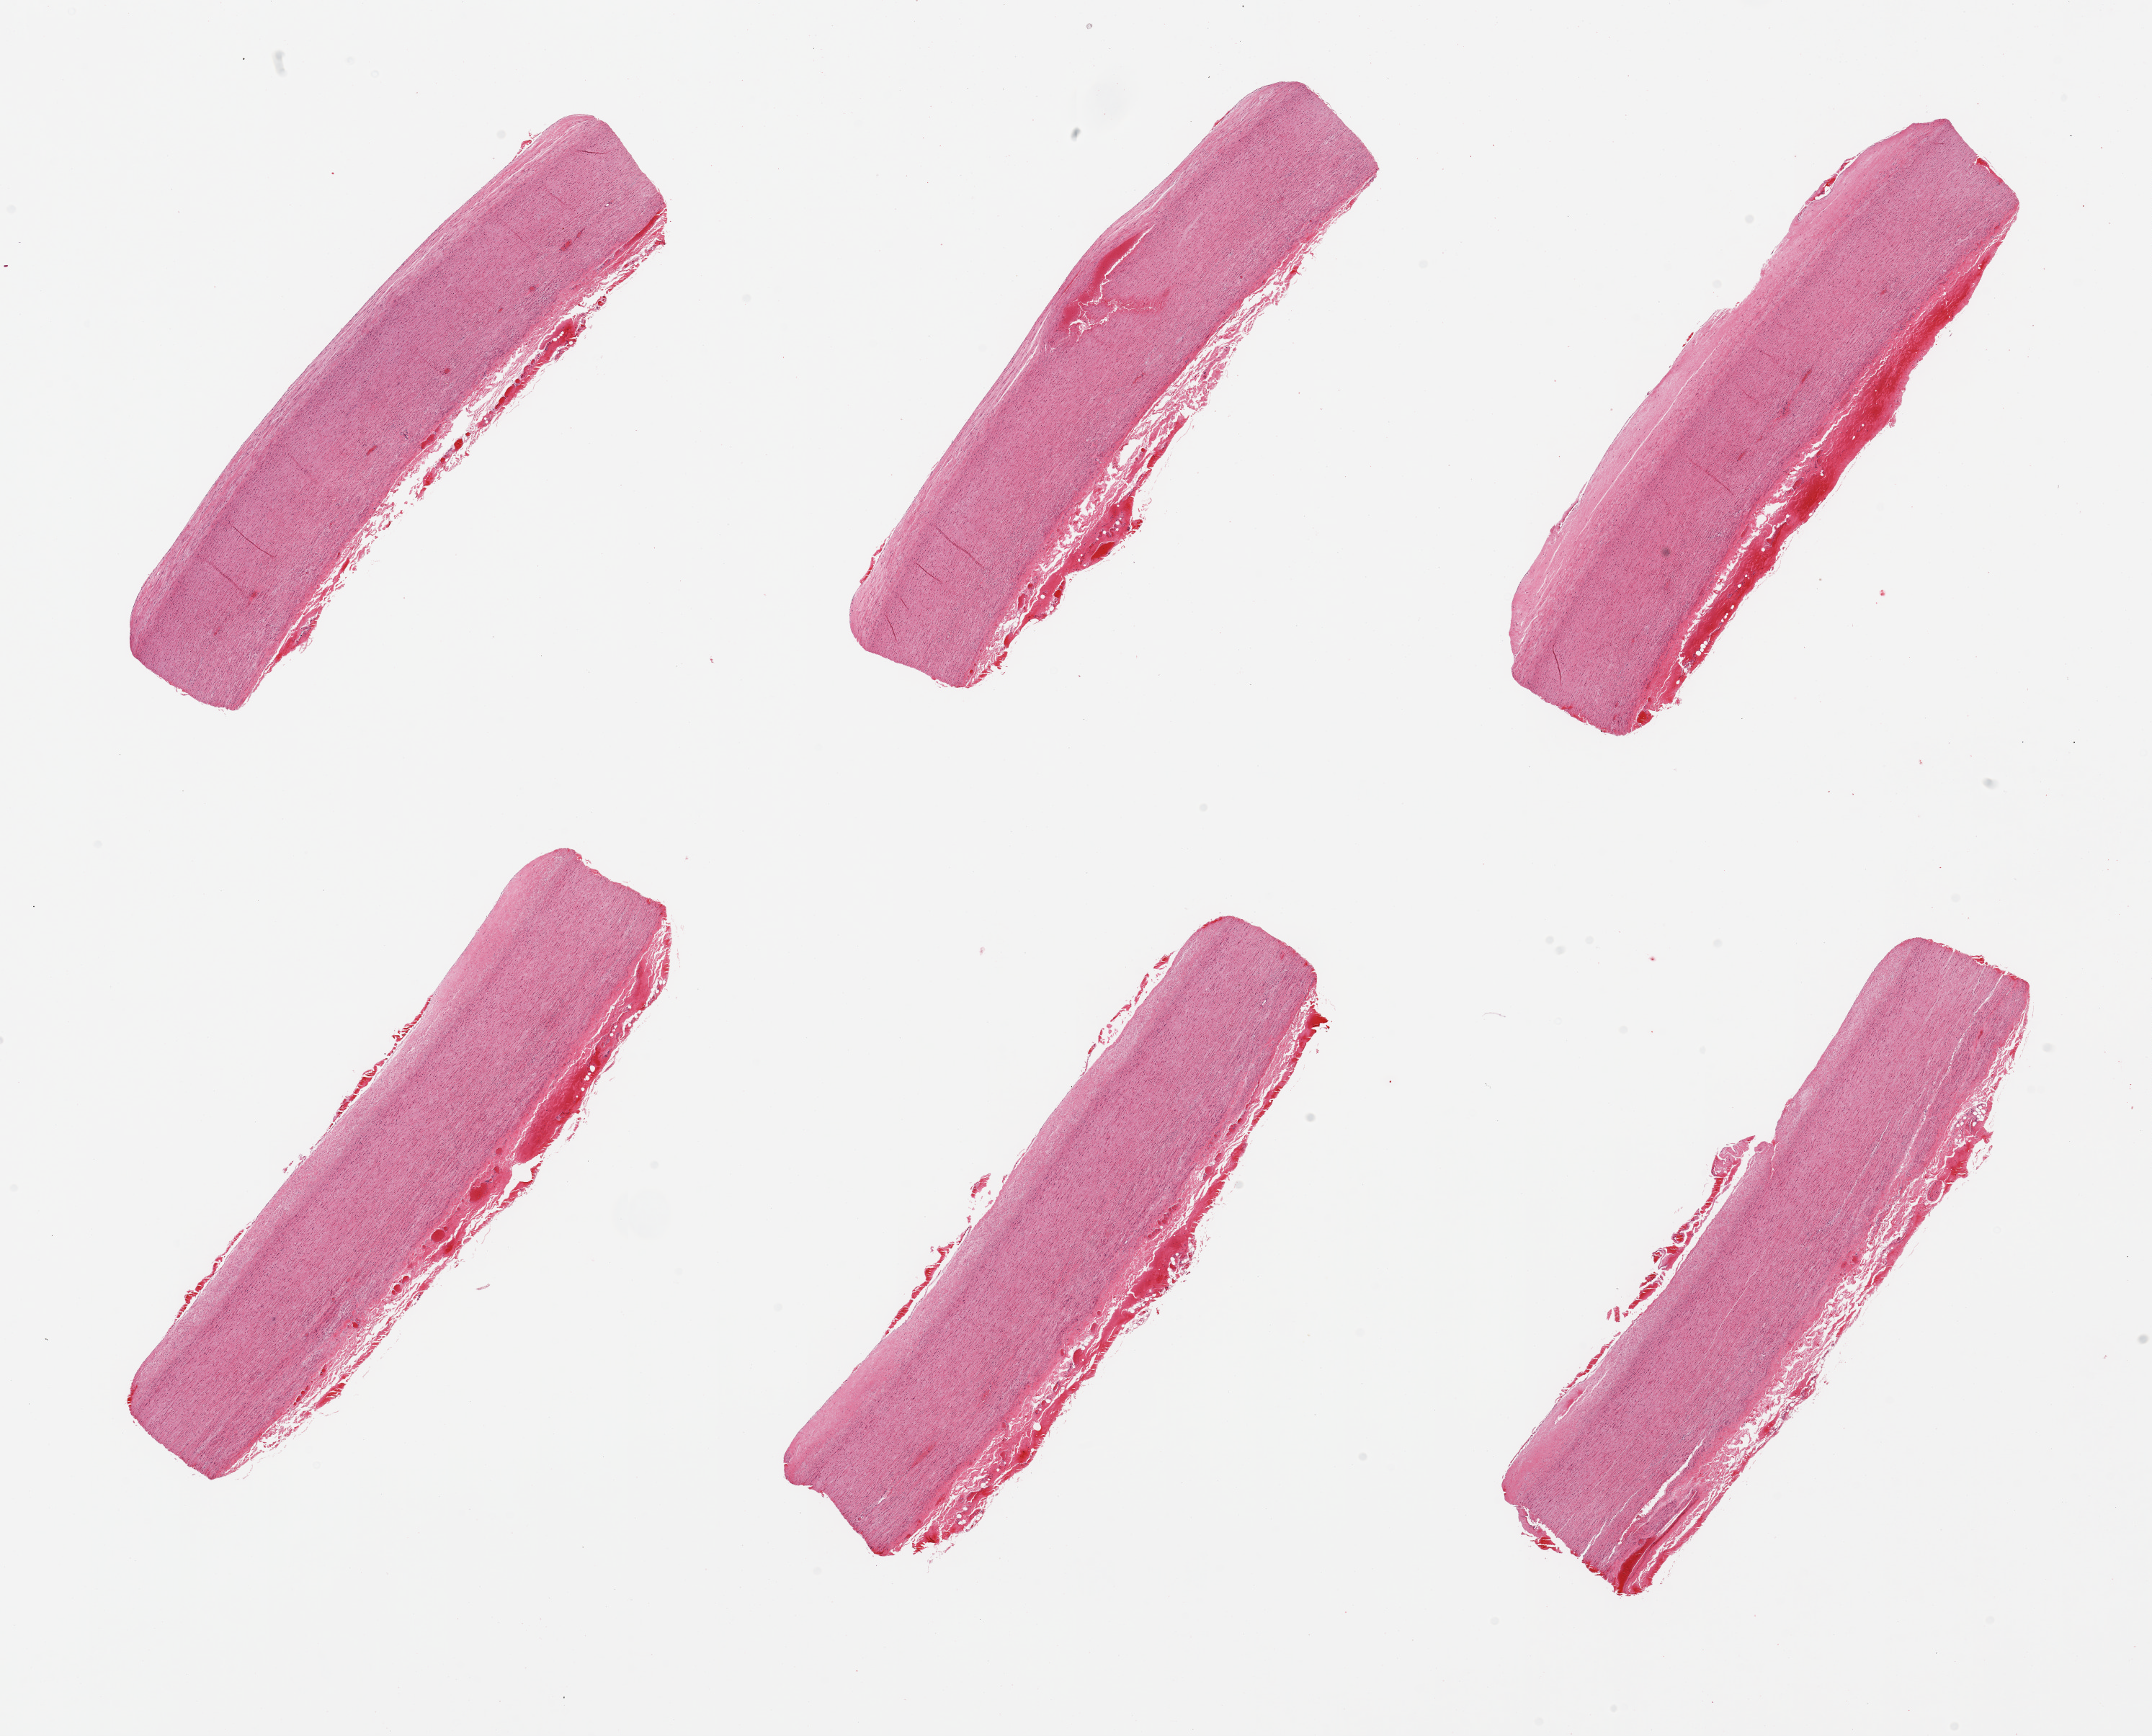
Whole-slide image, haematoxylin and eosin stain — whole scanned area (about 23.6 x 19.1 mm) shown as a low-resolution overview. PAXgene-fixed, paraffin-embedded tissue. Sampled site (target tissue): aorta. Donor tissue sample.
- pathologist's review note for this sample: 6 pieces; flat atherosclerosis and focal dissection of media with fresh hemorrhage; congested adventitia